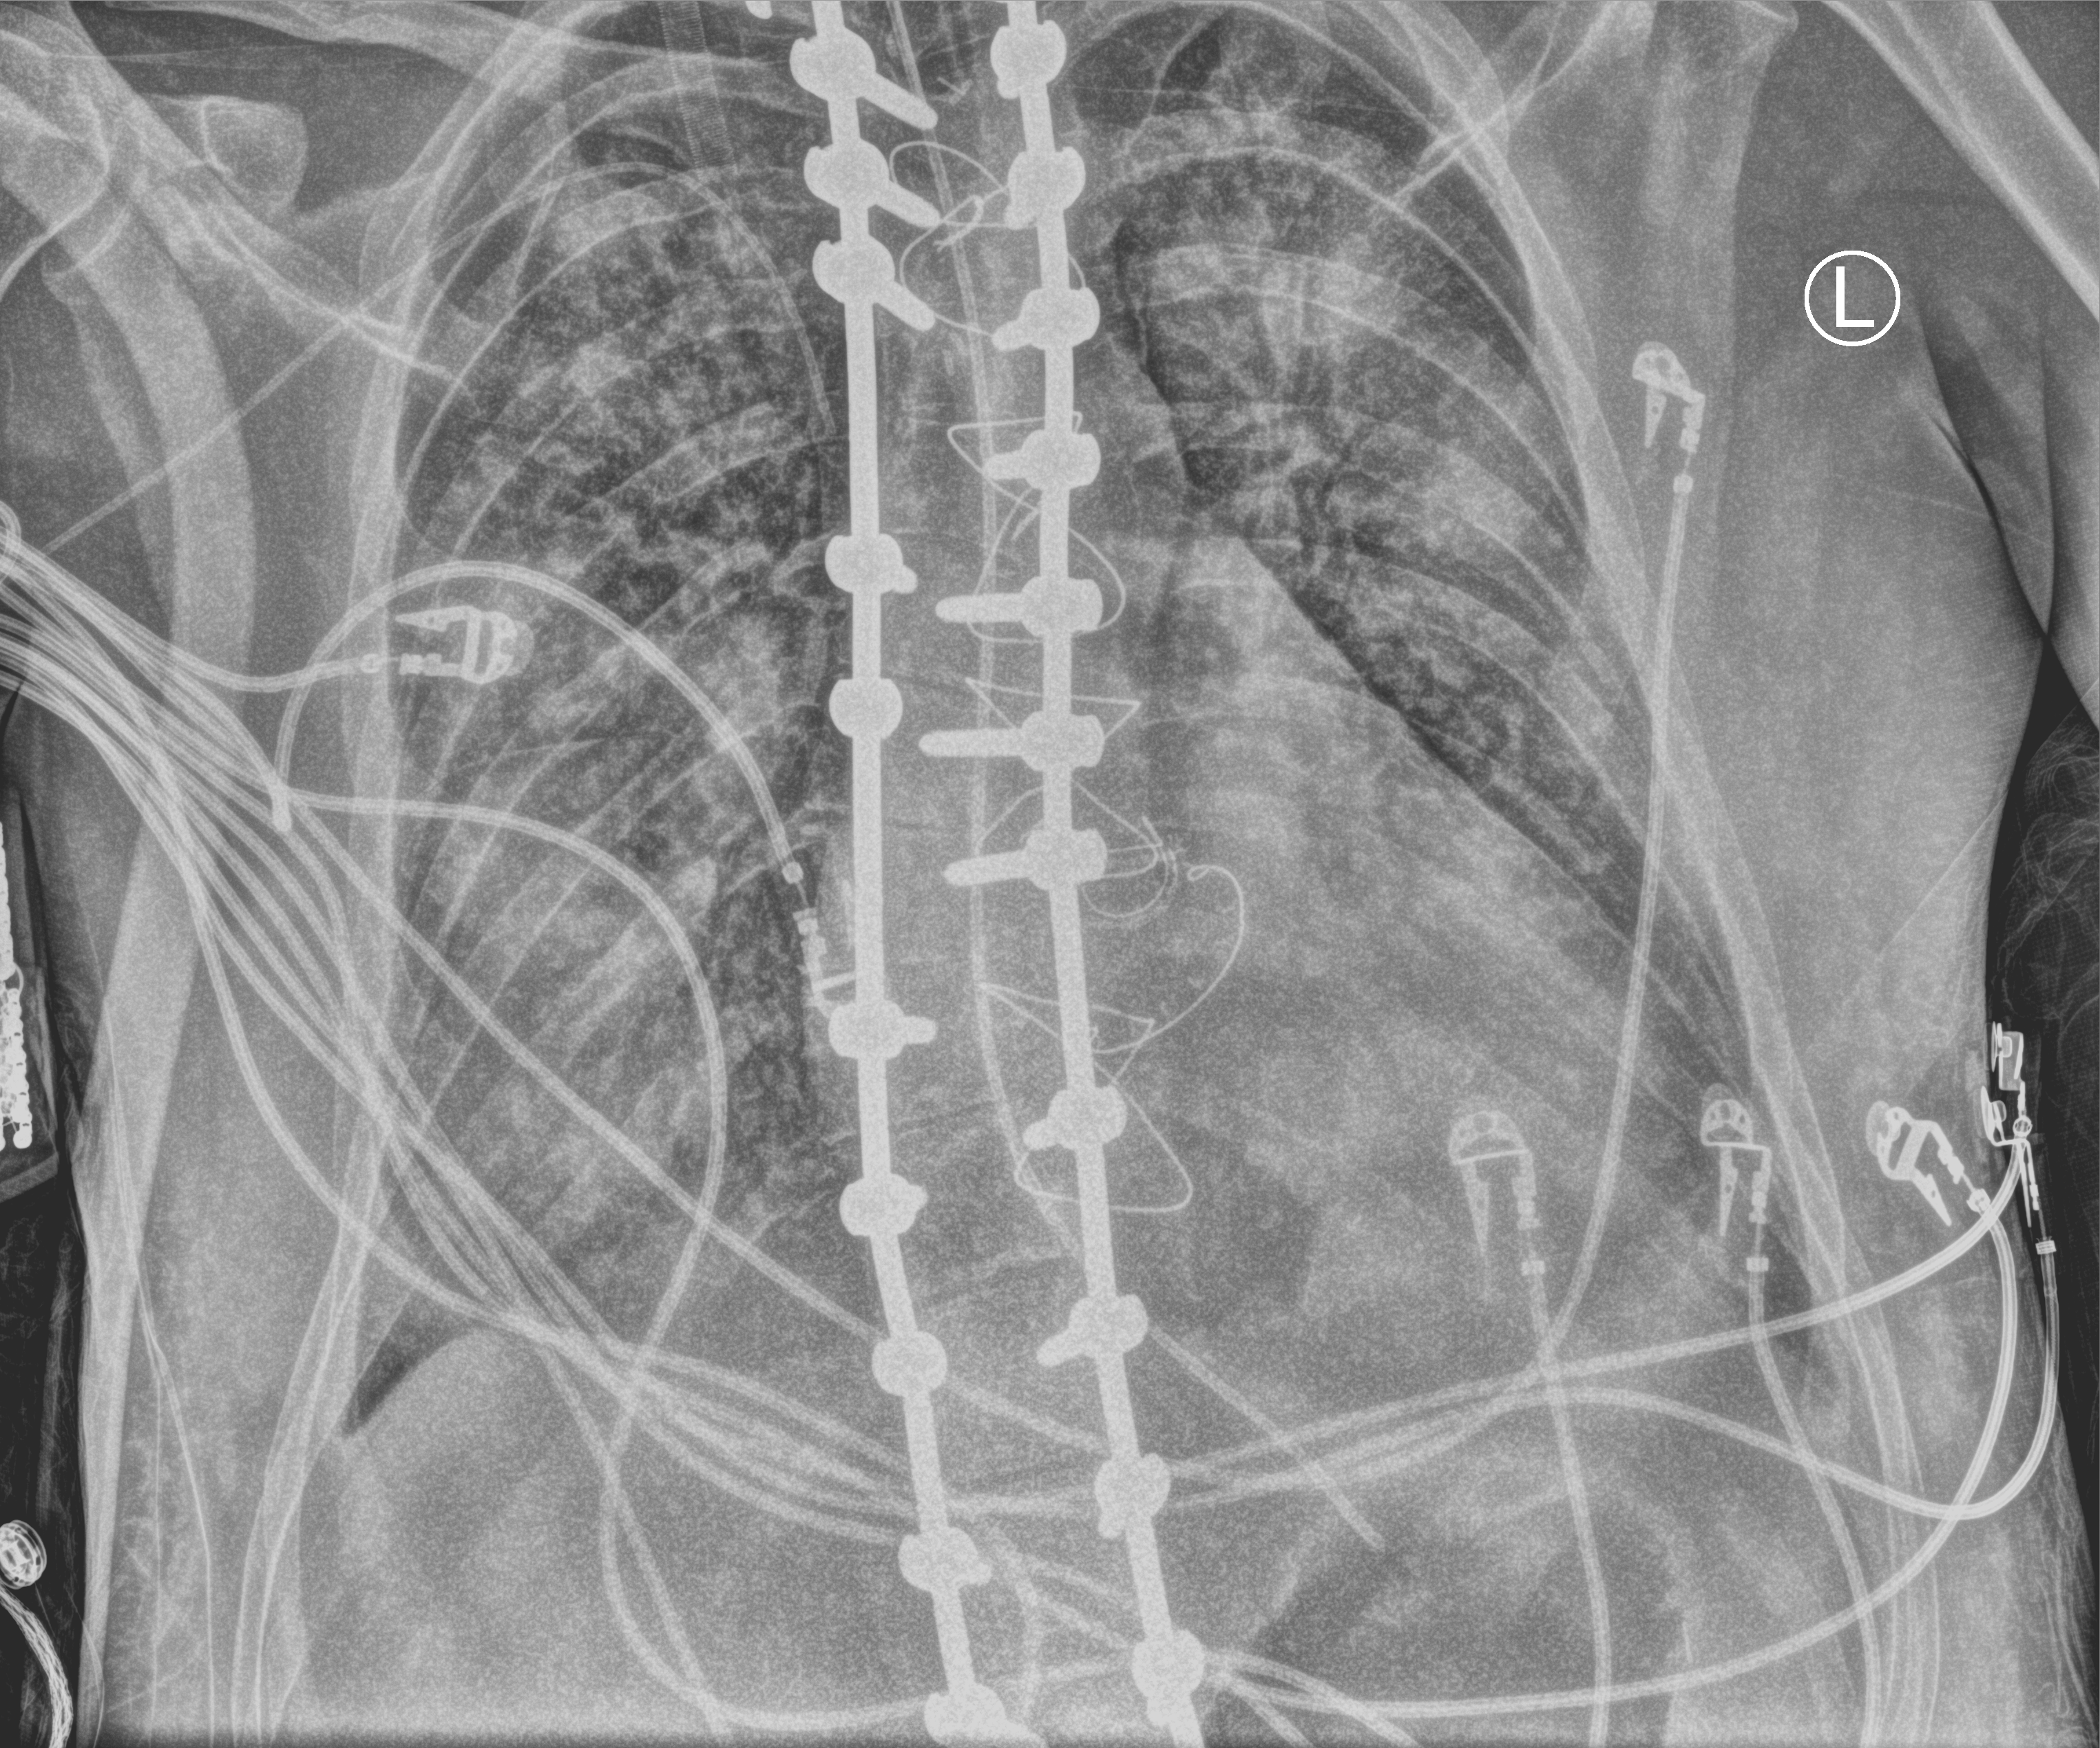
Chest radiograph; anteroposterior (AP) projection. Adult patient hospitalised with COVID-19, age 18–59 years.
Hospital-stay facts (about this admission, not read from this image; timing relative to this image not recorded): mechanically ventilated during this hospital stay: yes.